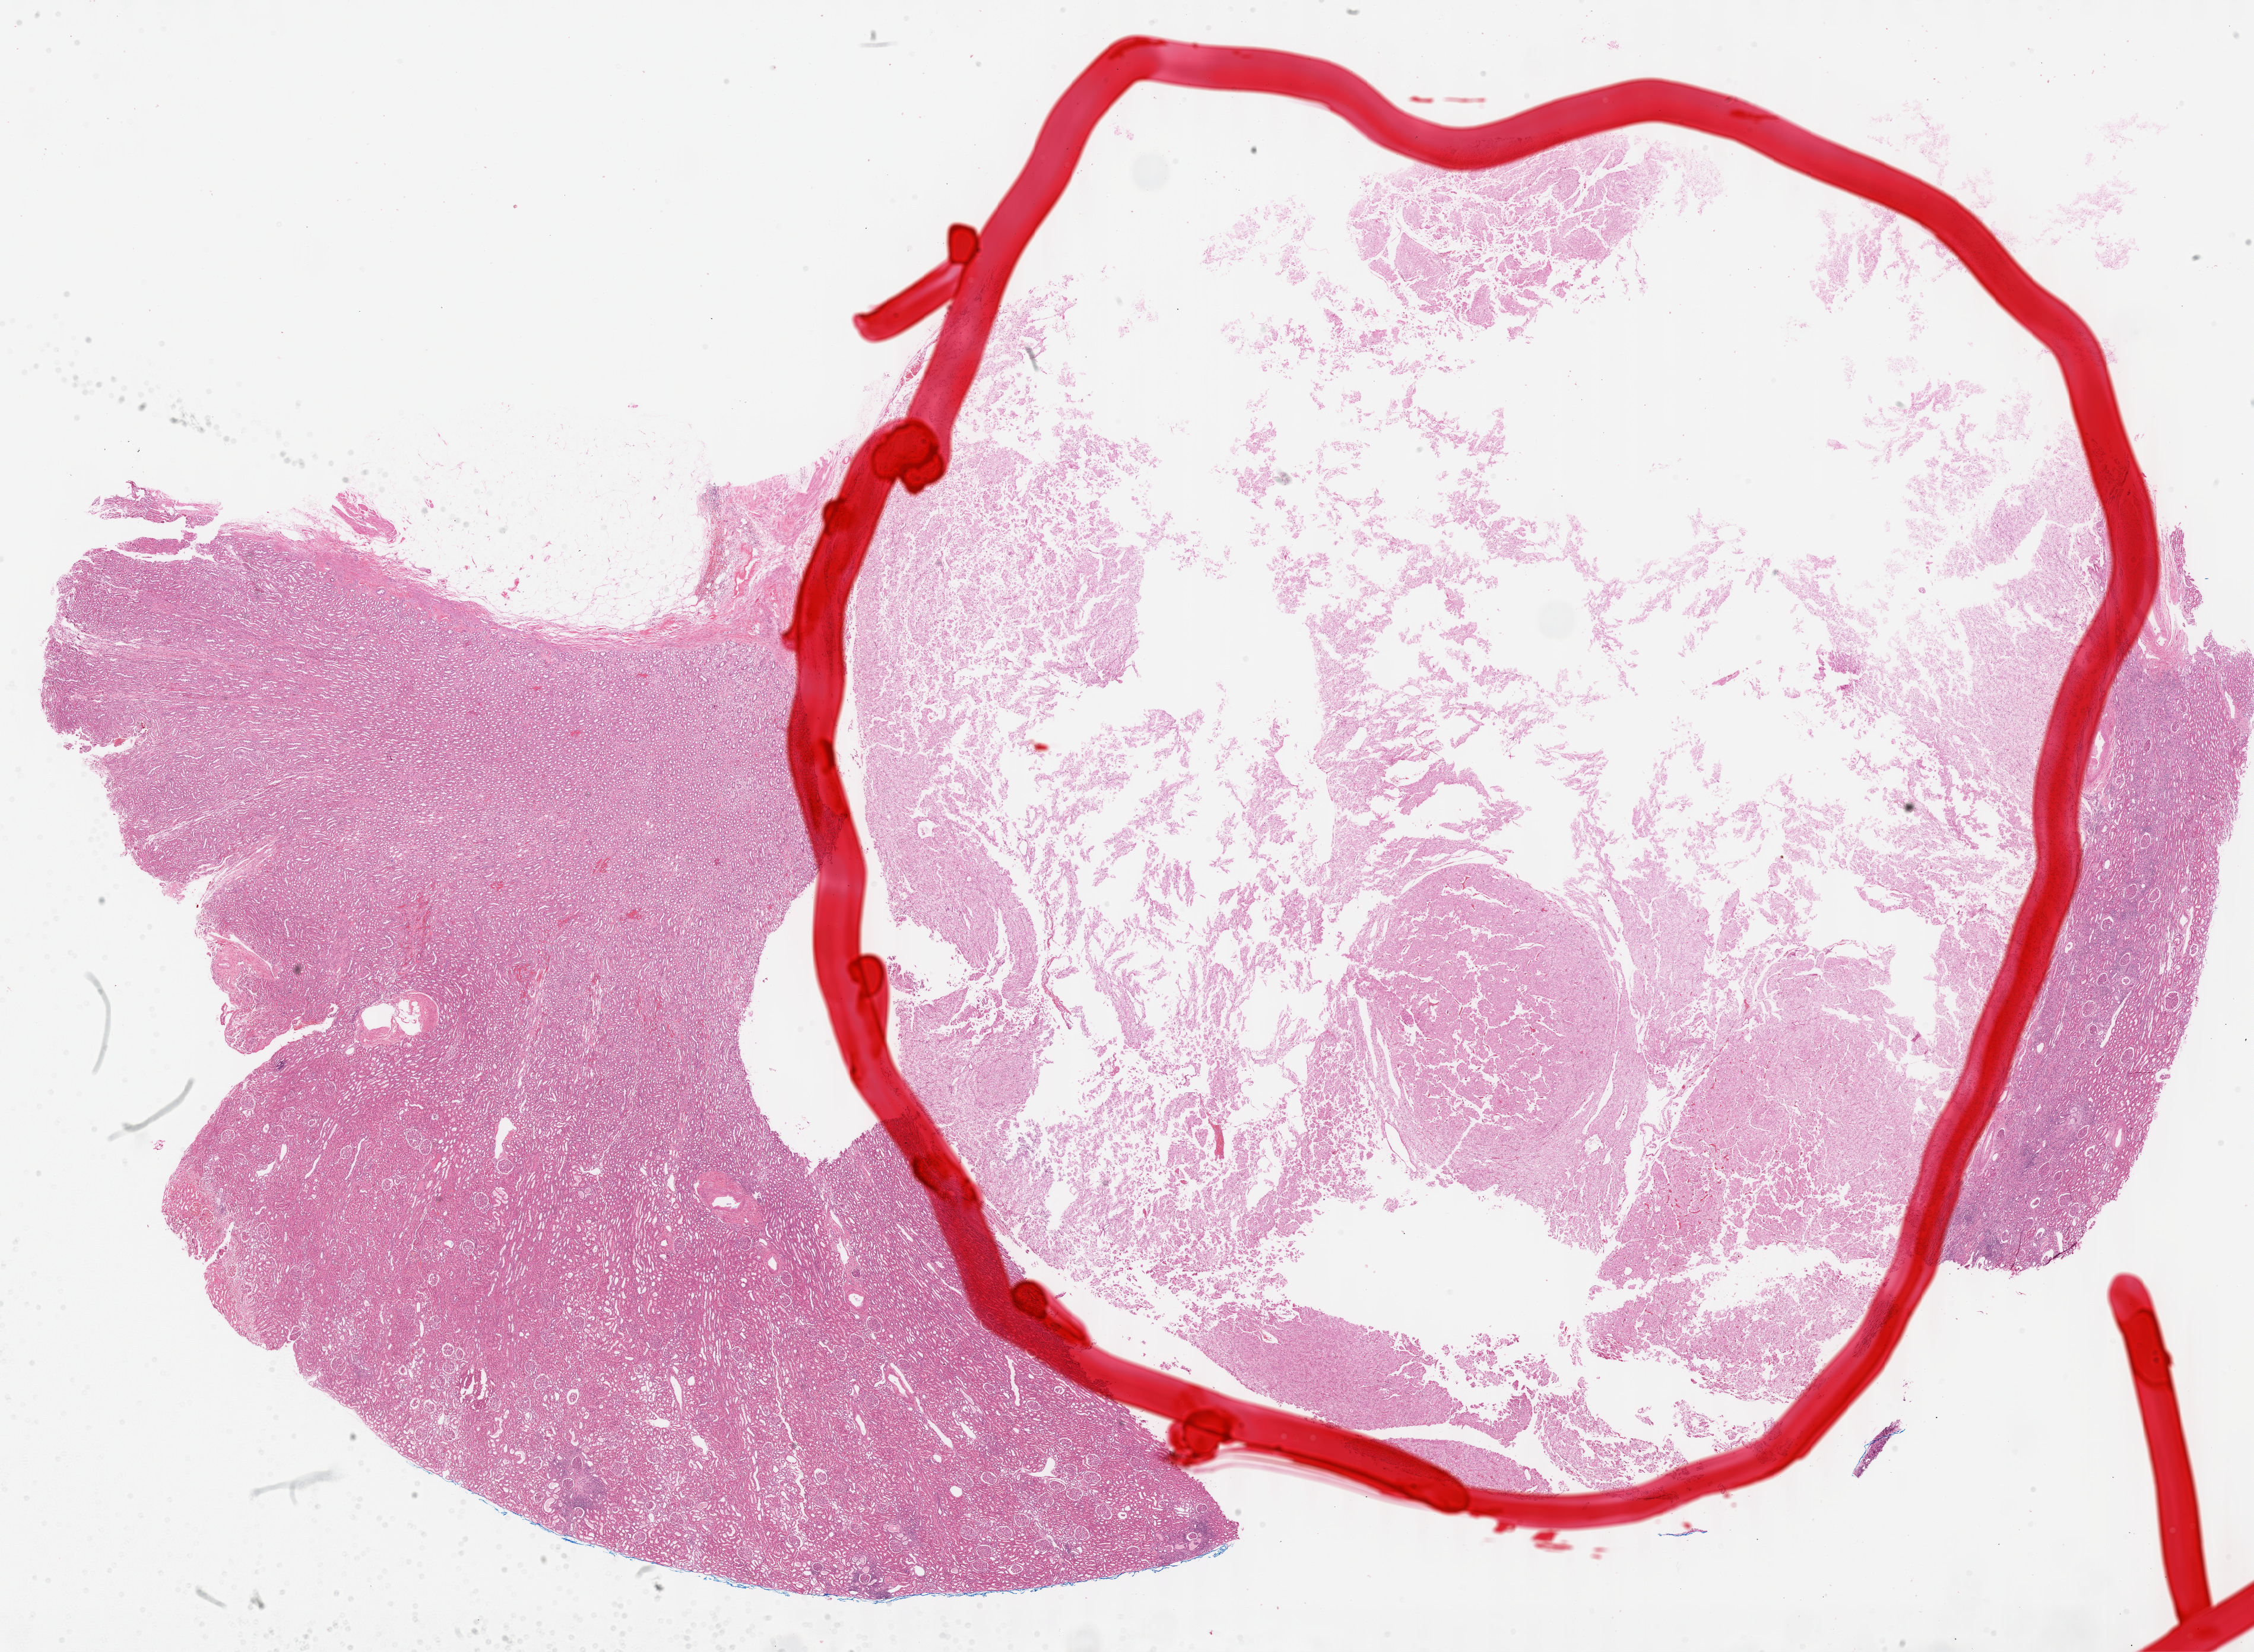
H&E-stained whole-slide image — whole scanned area (about 30.7 x 22.5 mm, acquisition: 40x scan) shown as a low-resolution overview. Formalin-fixed paraffin-embedded (FFPE) diagnostic section. Kidney, primary tumour sample. Female patient; age at initial diagnosis 55 years. Pathologist review of this section (percent, as recorded): tumour cells 95%, tumour nuclei 97%, normal cells 0%, stromal cells 5%, necrosis 0%. Infiltration values recorded for this section: lymphocyte infiltration 1%, monocyte infiltration 1%, neutrophil infiltration 0%.
AJCC pathologic stage: I. Lymph nodes positive (case pathology): 0 of 36 examined. Histologic diagnosis: Renal cell carcinoma, chromophobe type.